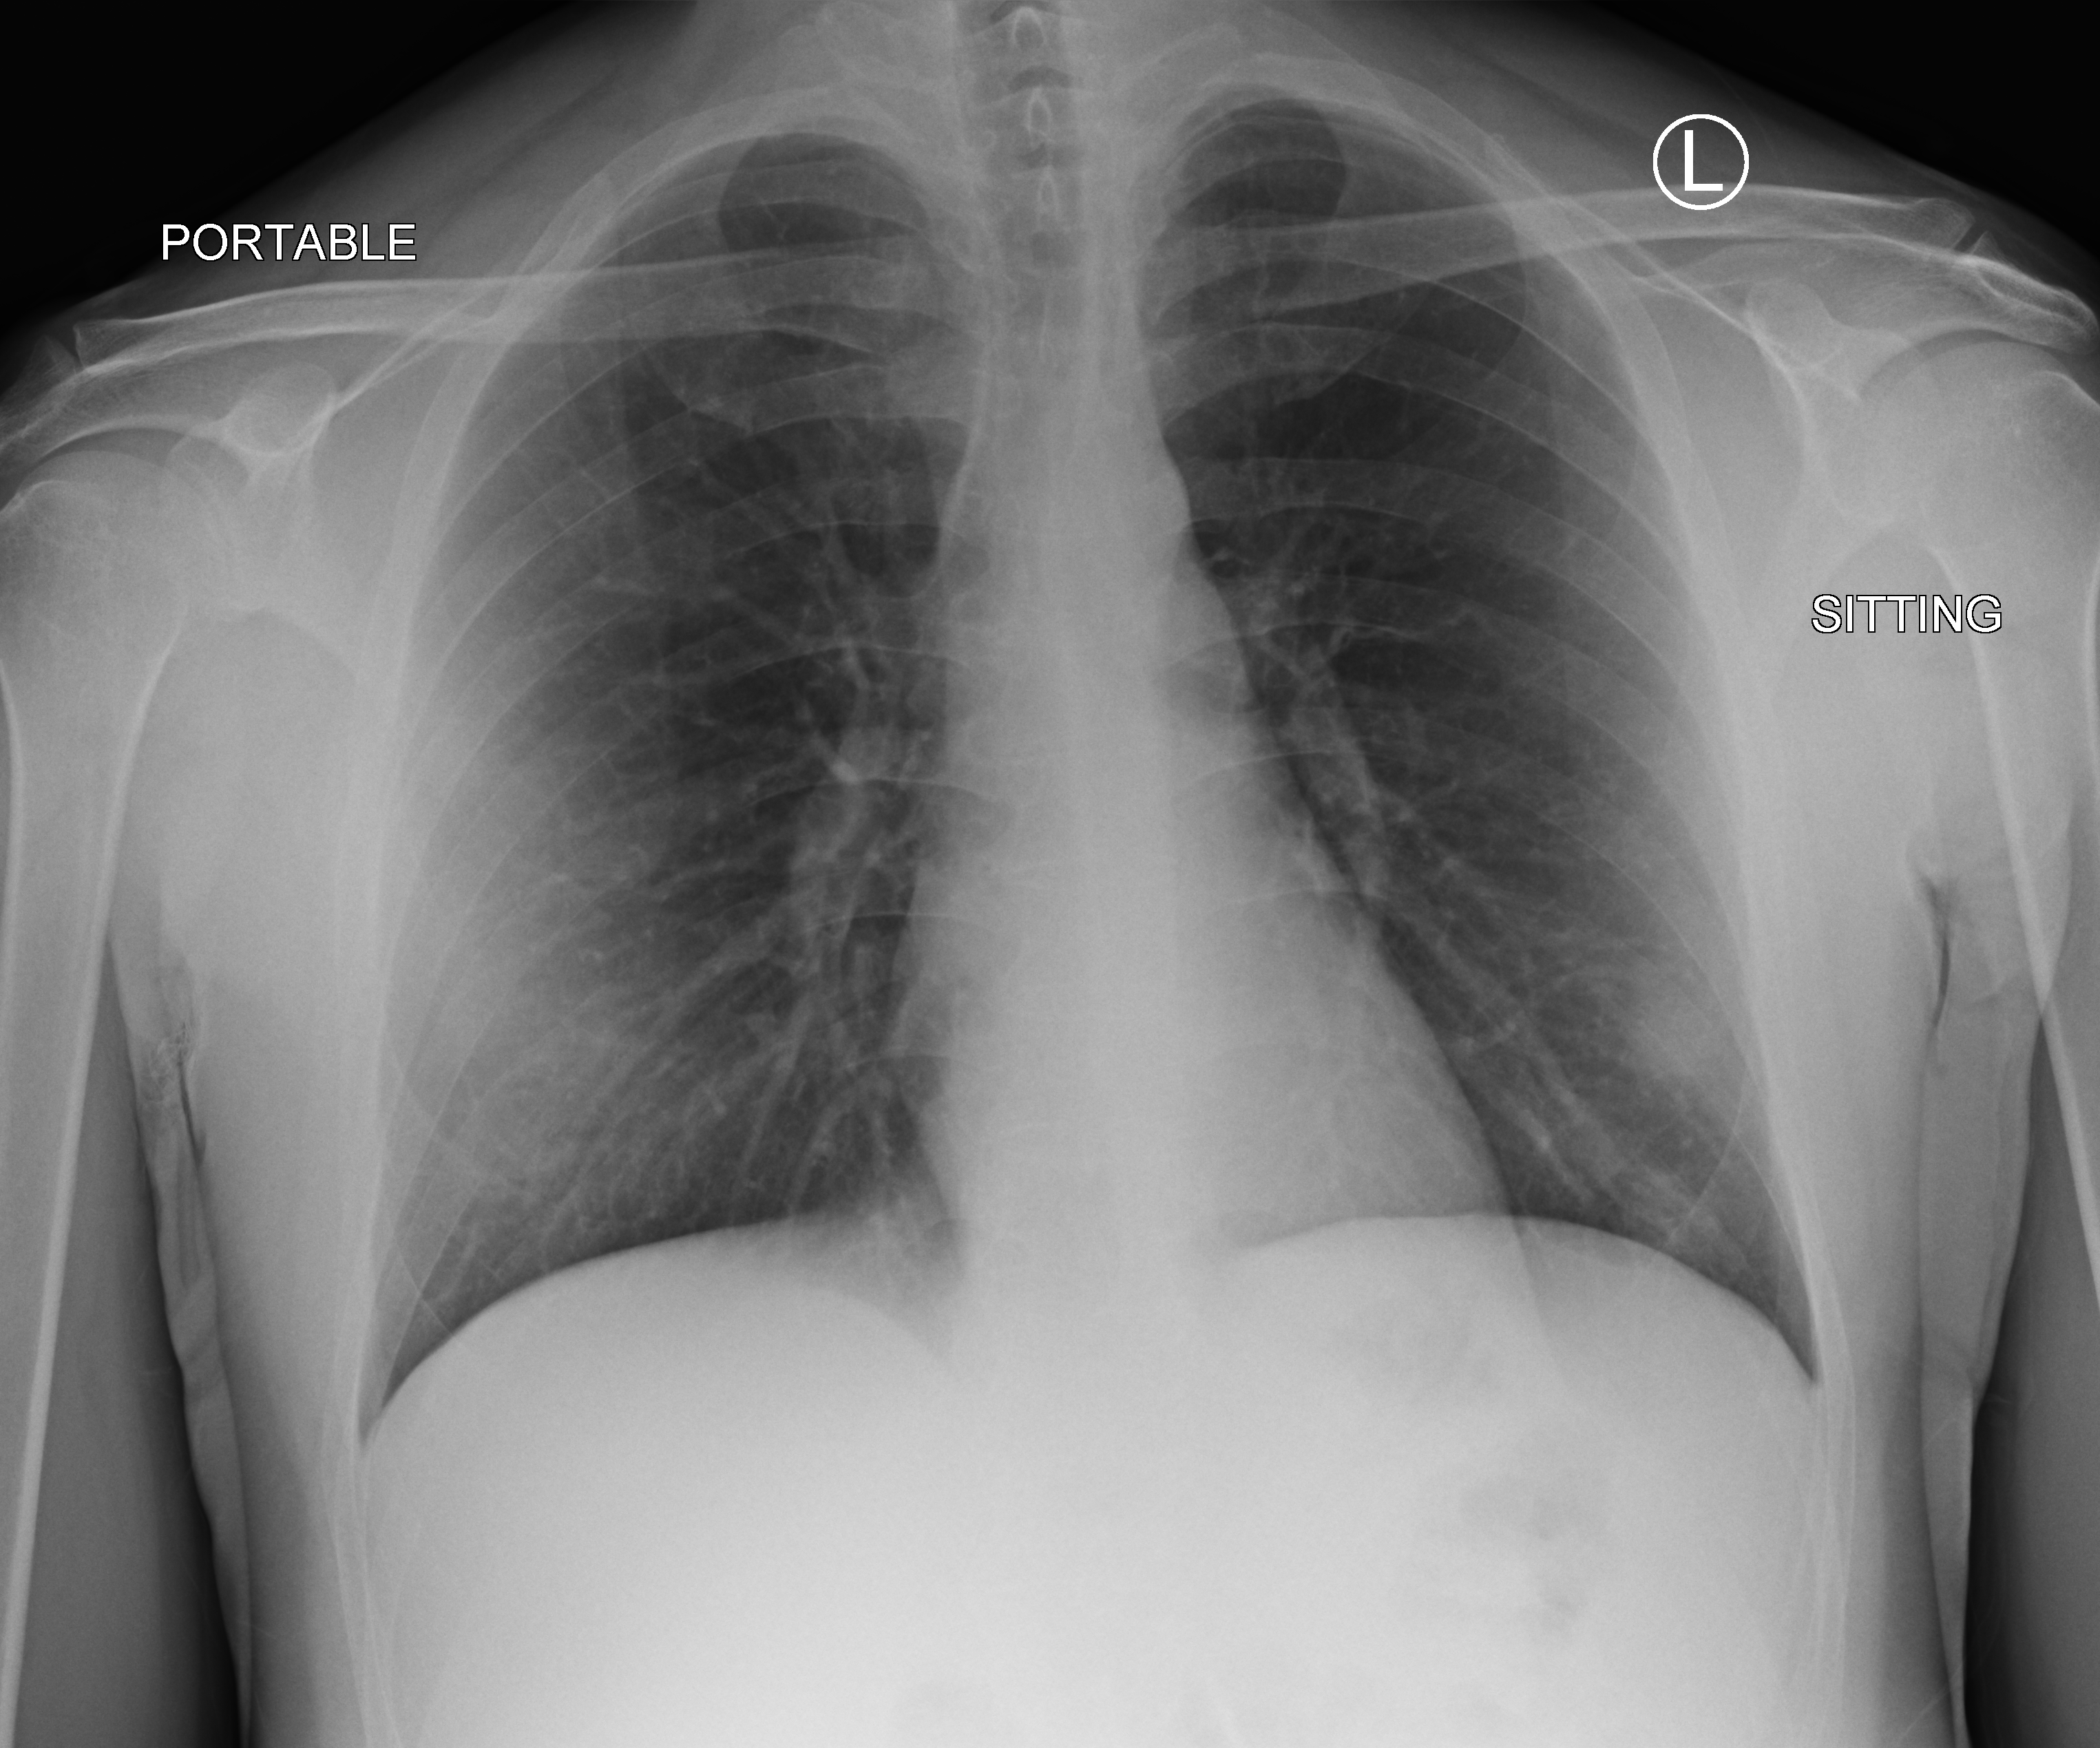
Portable chest radiograph; anteroposterior (AP) projection. Patient hospitalised with COVID-19; male, aged 18–59 years.
Hospital-stay facts (about this admission, not read from this image; timing relative to this image not recorded): mechanically ventilated during this hospital stay: no; diabetes (admission record): no.